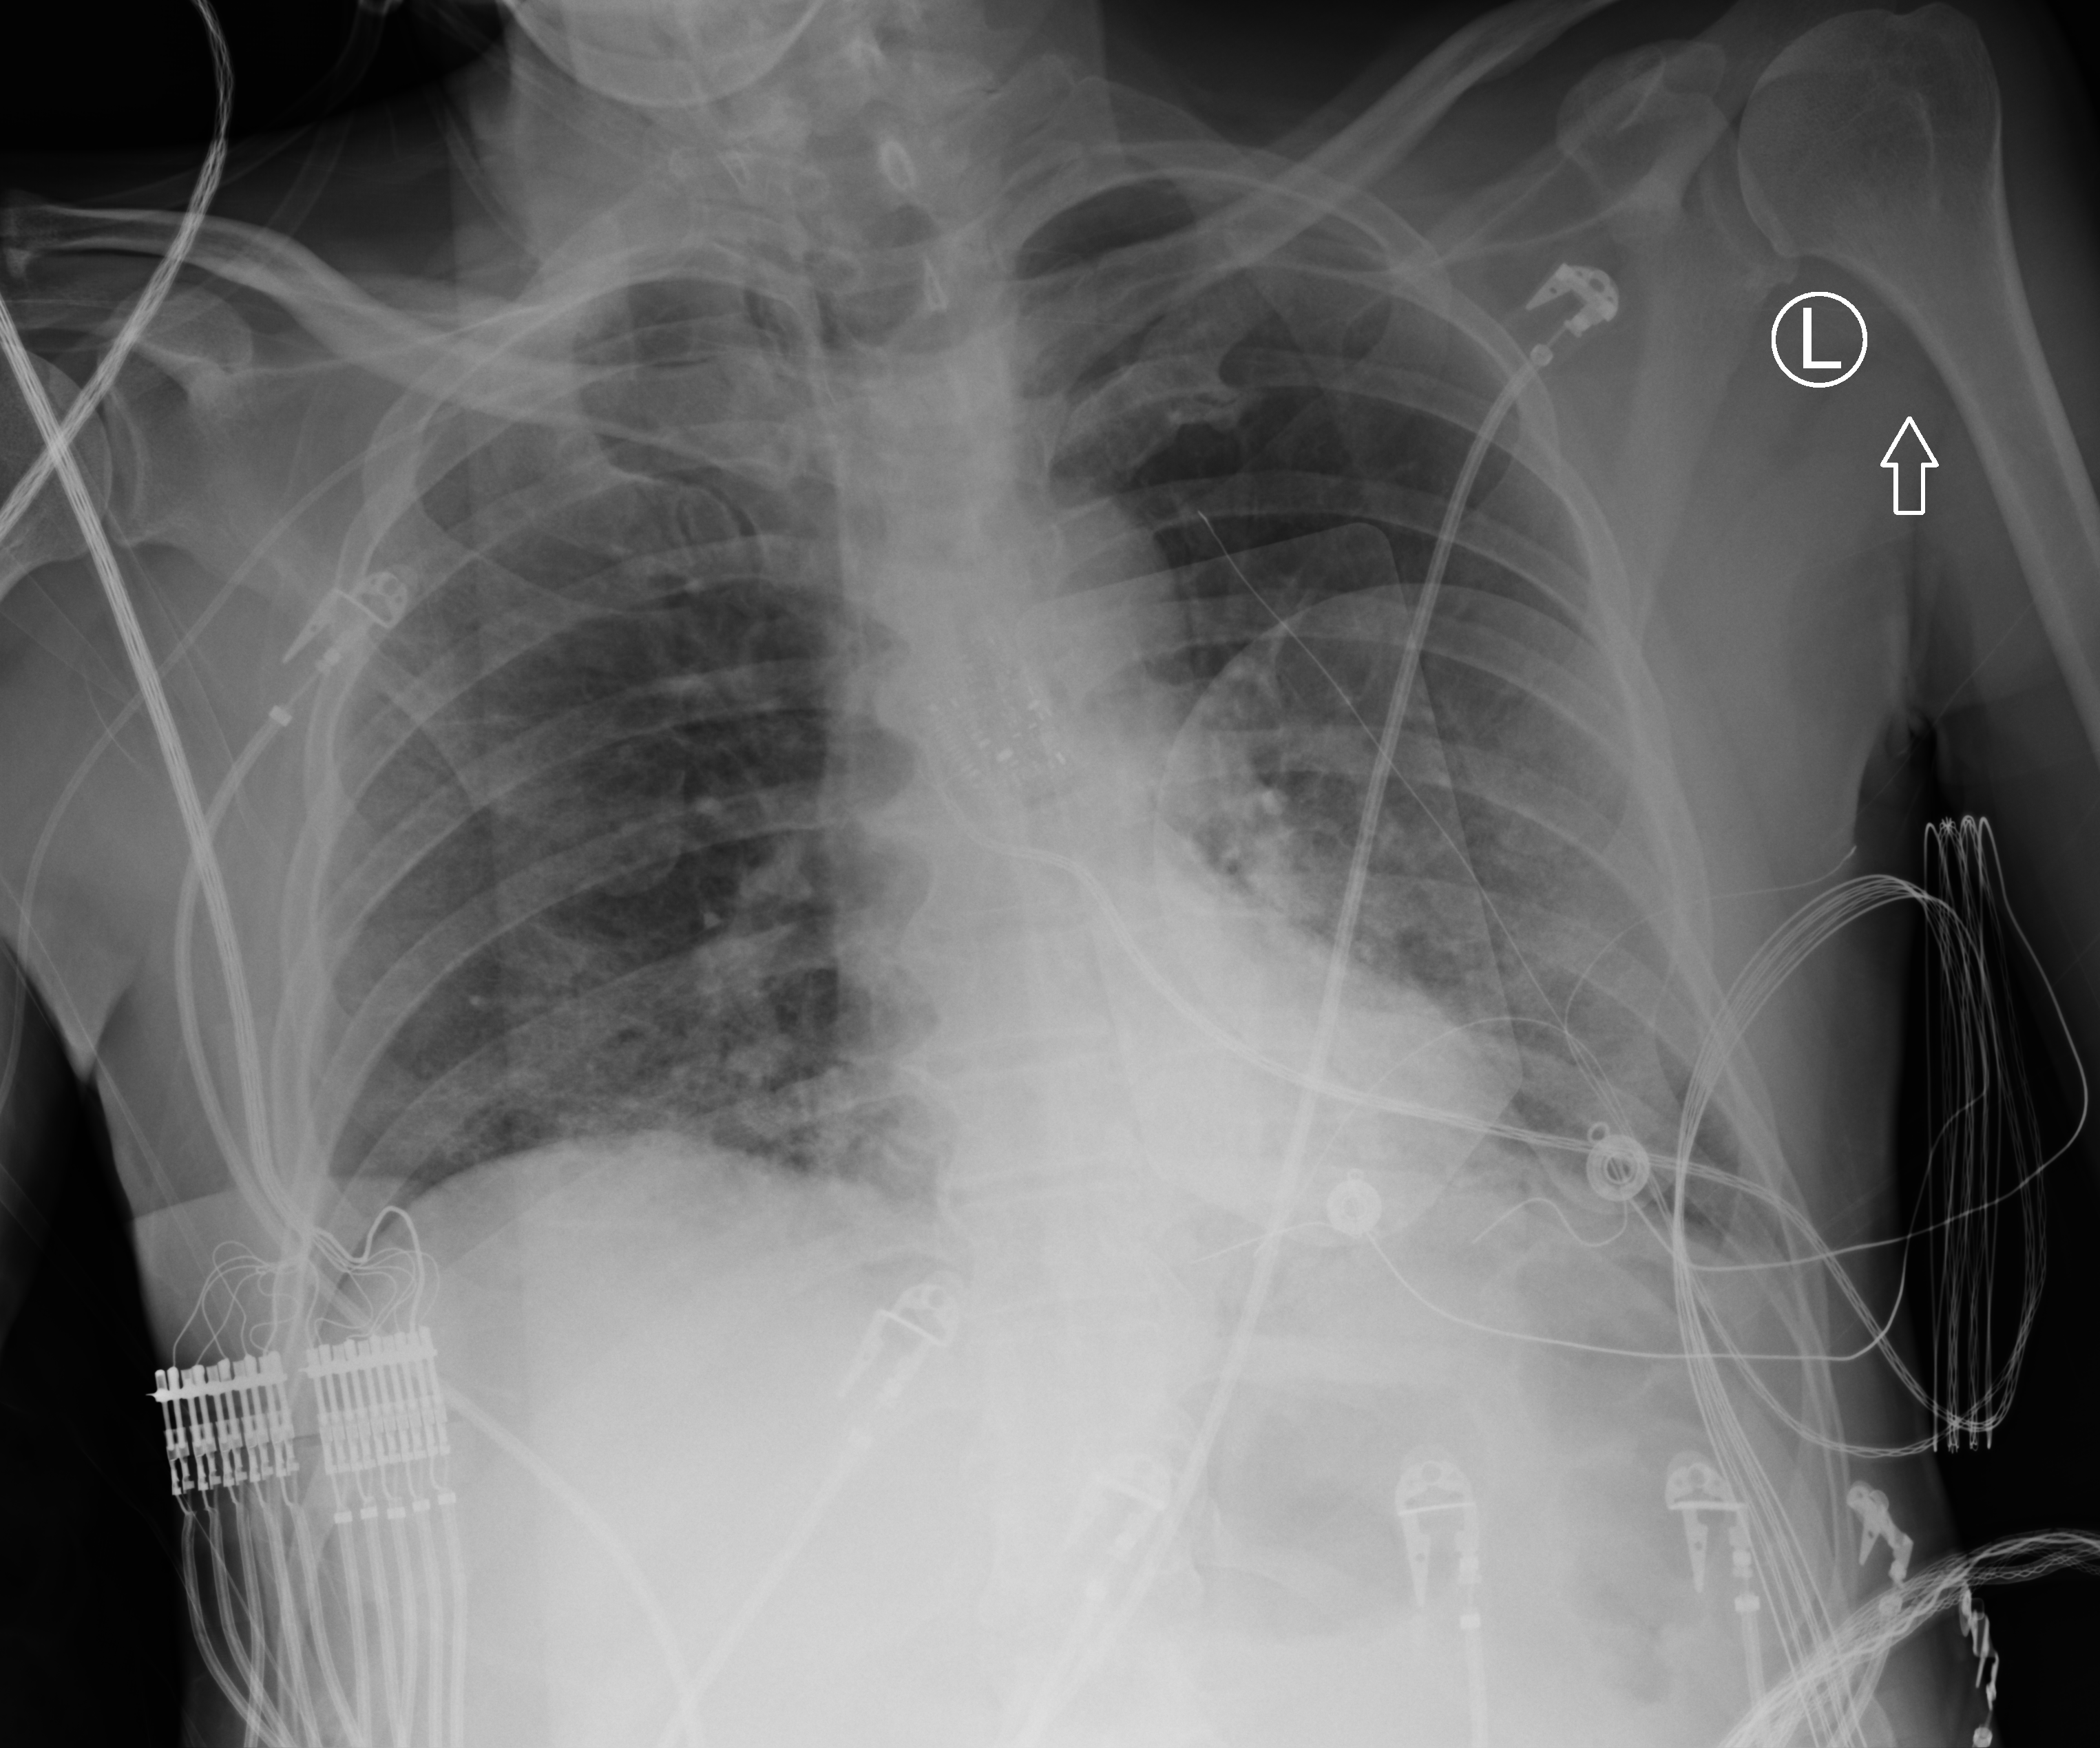
Portable chest radiograph. Male patient hospitalised with COVID-19, age 60–74 years.
Admission-level facts for this patient (not findings on this image; timing relative to this image not recorded):
- chronic kidney disease (admission record): no